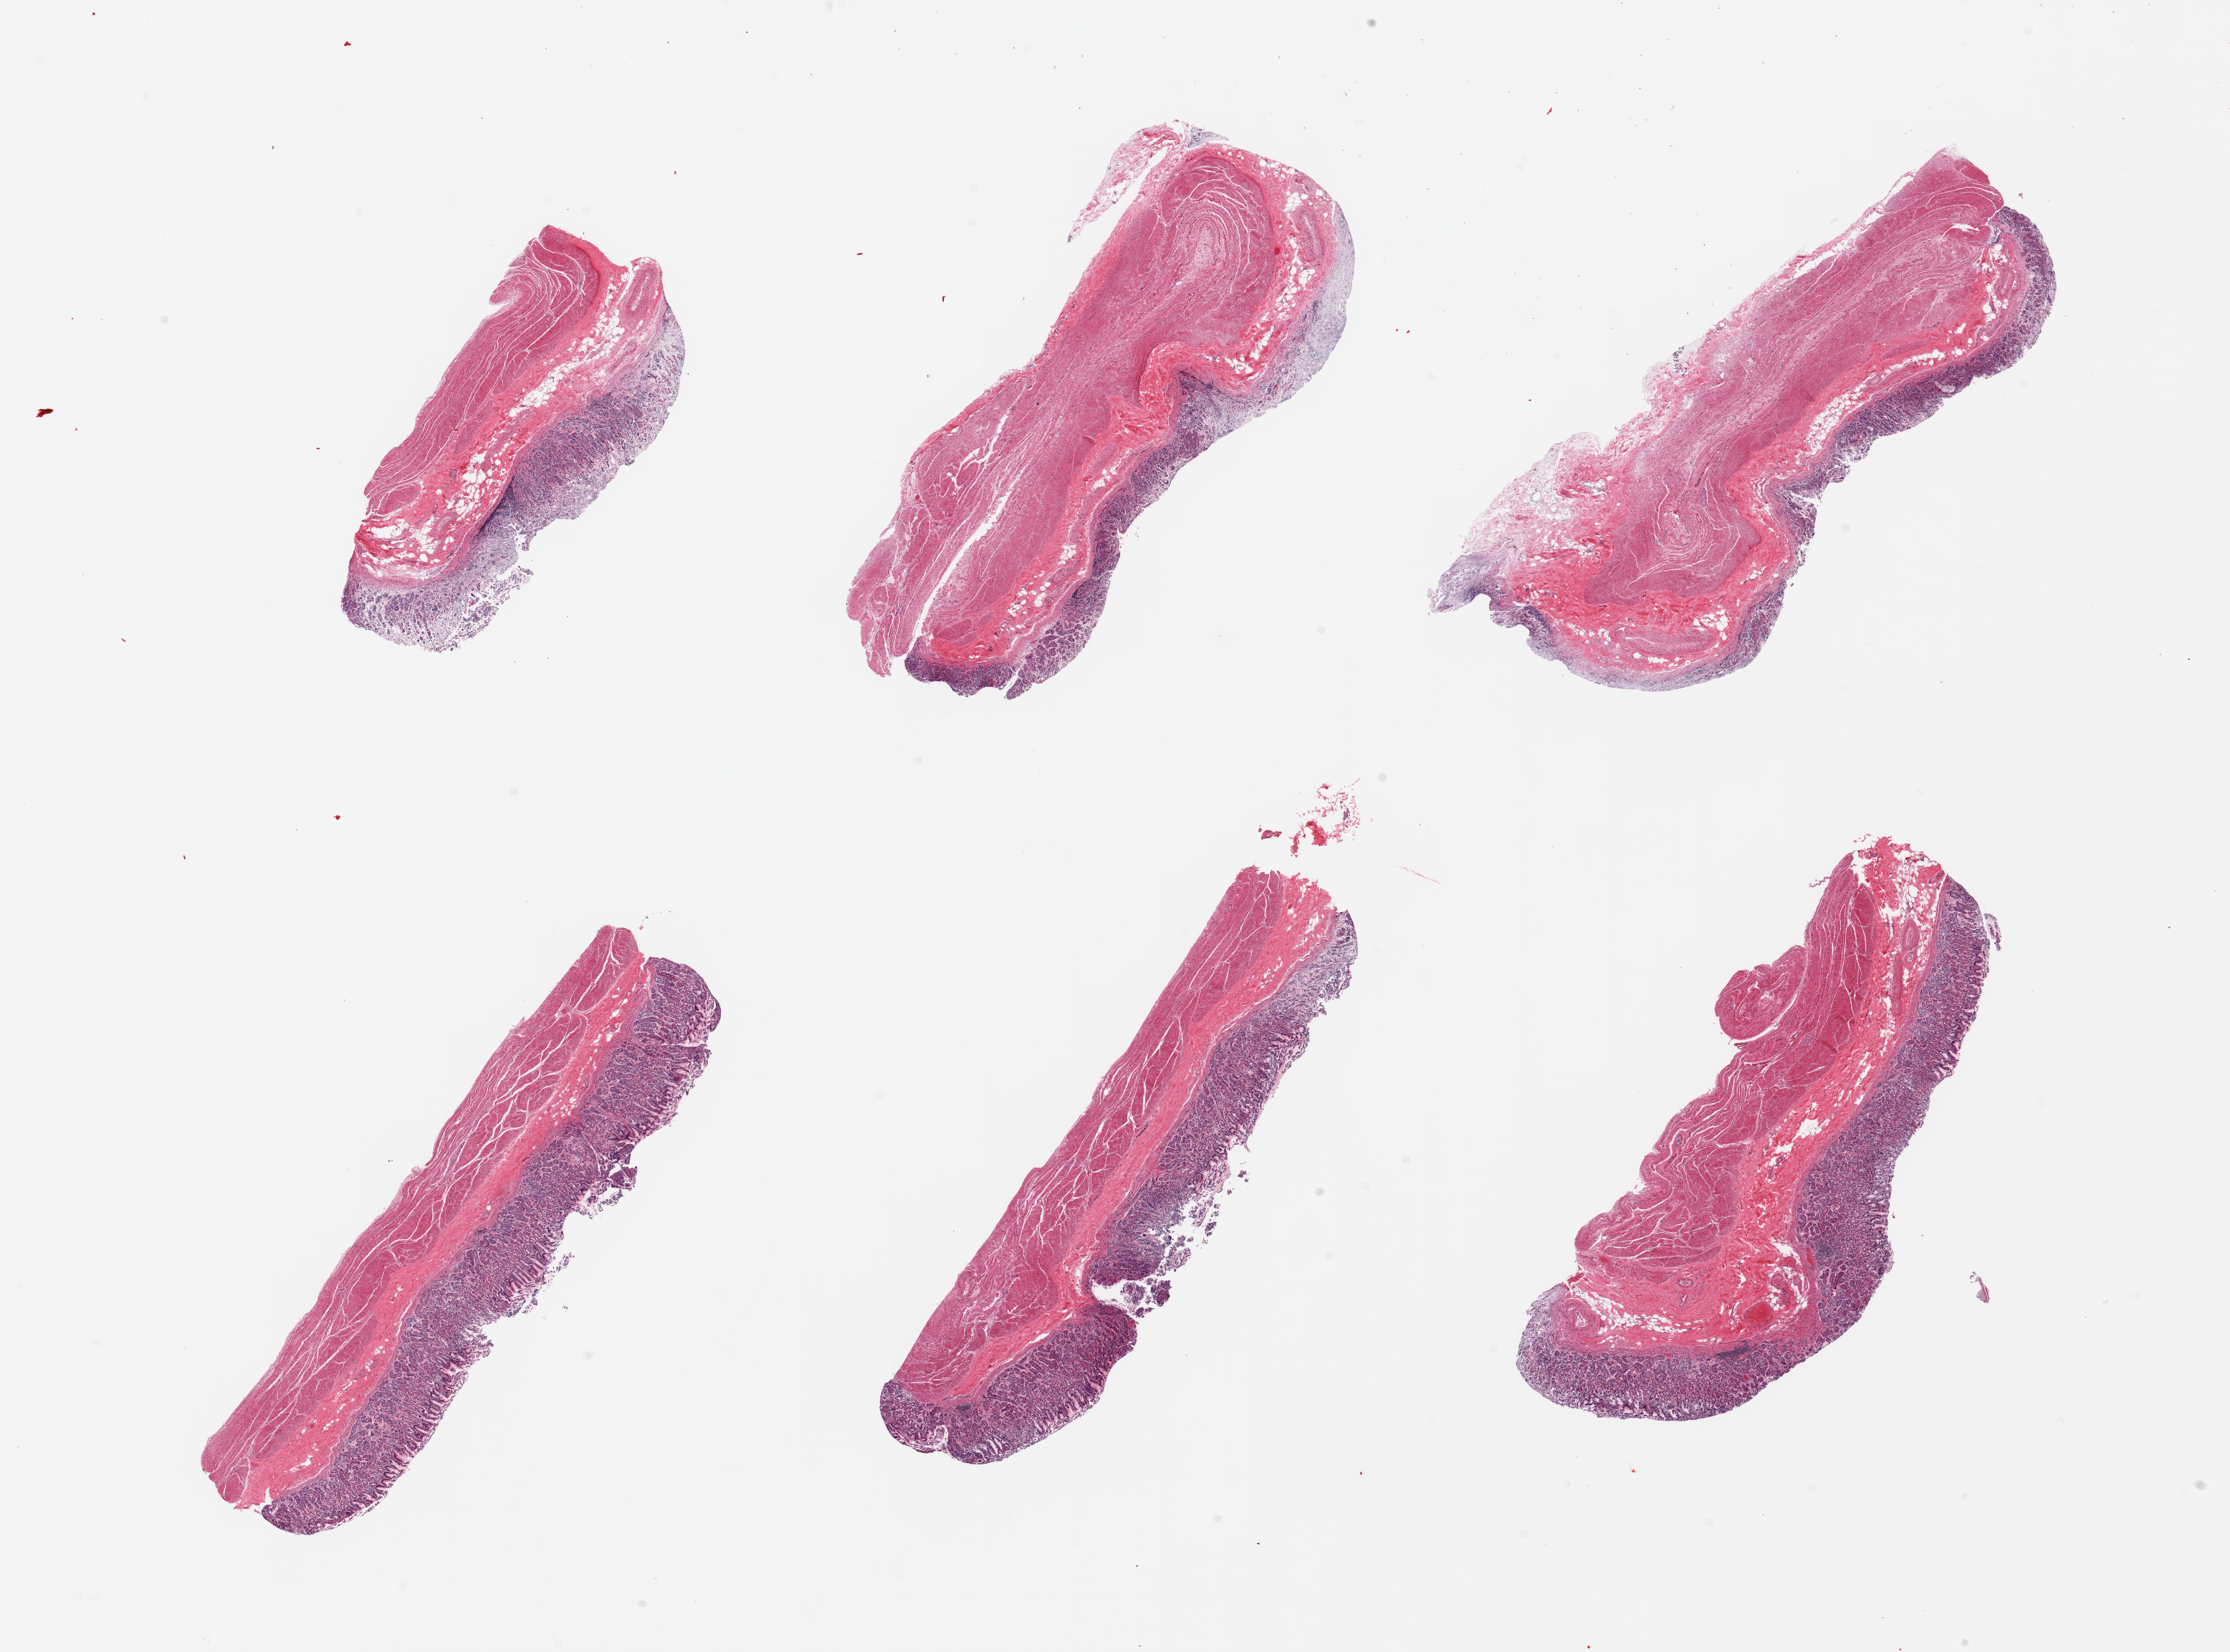
Digitized H&E-stained section, a low-resolution overview of the entire scanned area, about 24.6 x 18.2 mm, PAXgene-fixed, paraffin-embedded tissue, sampled site (target tissue): stomach, donor tissue sample. Donor sex: male.
Reviewer comment on this tissue sample: 6 pieces, mucosa up to ~0.7mm, 30-50% thickness, moderate-markedly advanced autolysis.